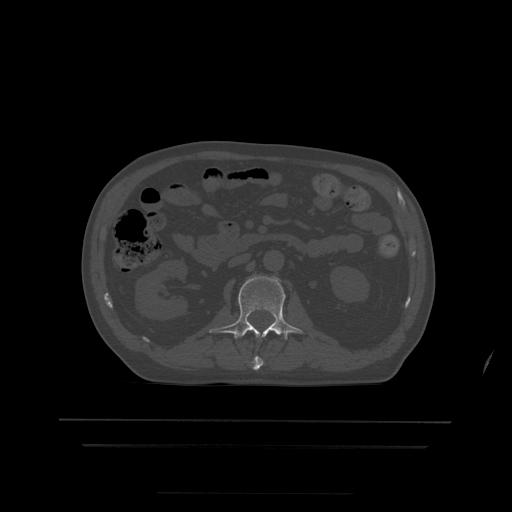
CT including the spine, one axial slice; position 147 of 522 along the scan axis; bone window (W 1800 / L 400 HU); 1.25 mm slice thickness; 512 × 512 image matrix. Patient age 68 years. From the clinical record (not read from this slice): primary cancer: urothelial.
Outlined on this slice (semi-automatically segmented with operator editing):
- L1 vertebra: bounding box [x1, y1, x2, y2] px = [252, 357, 264, 371]
- L2 vertebra: [210, 276, 304, 340]